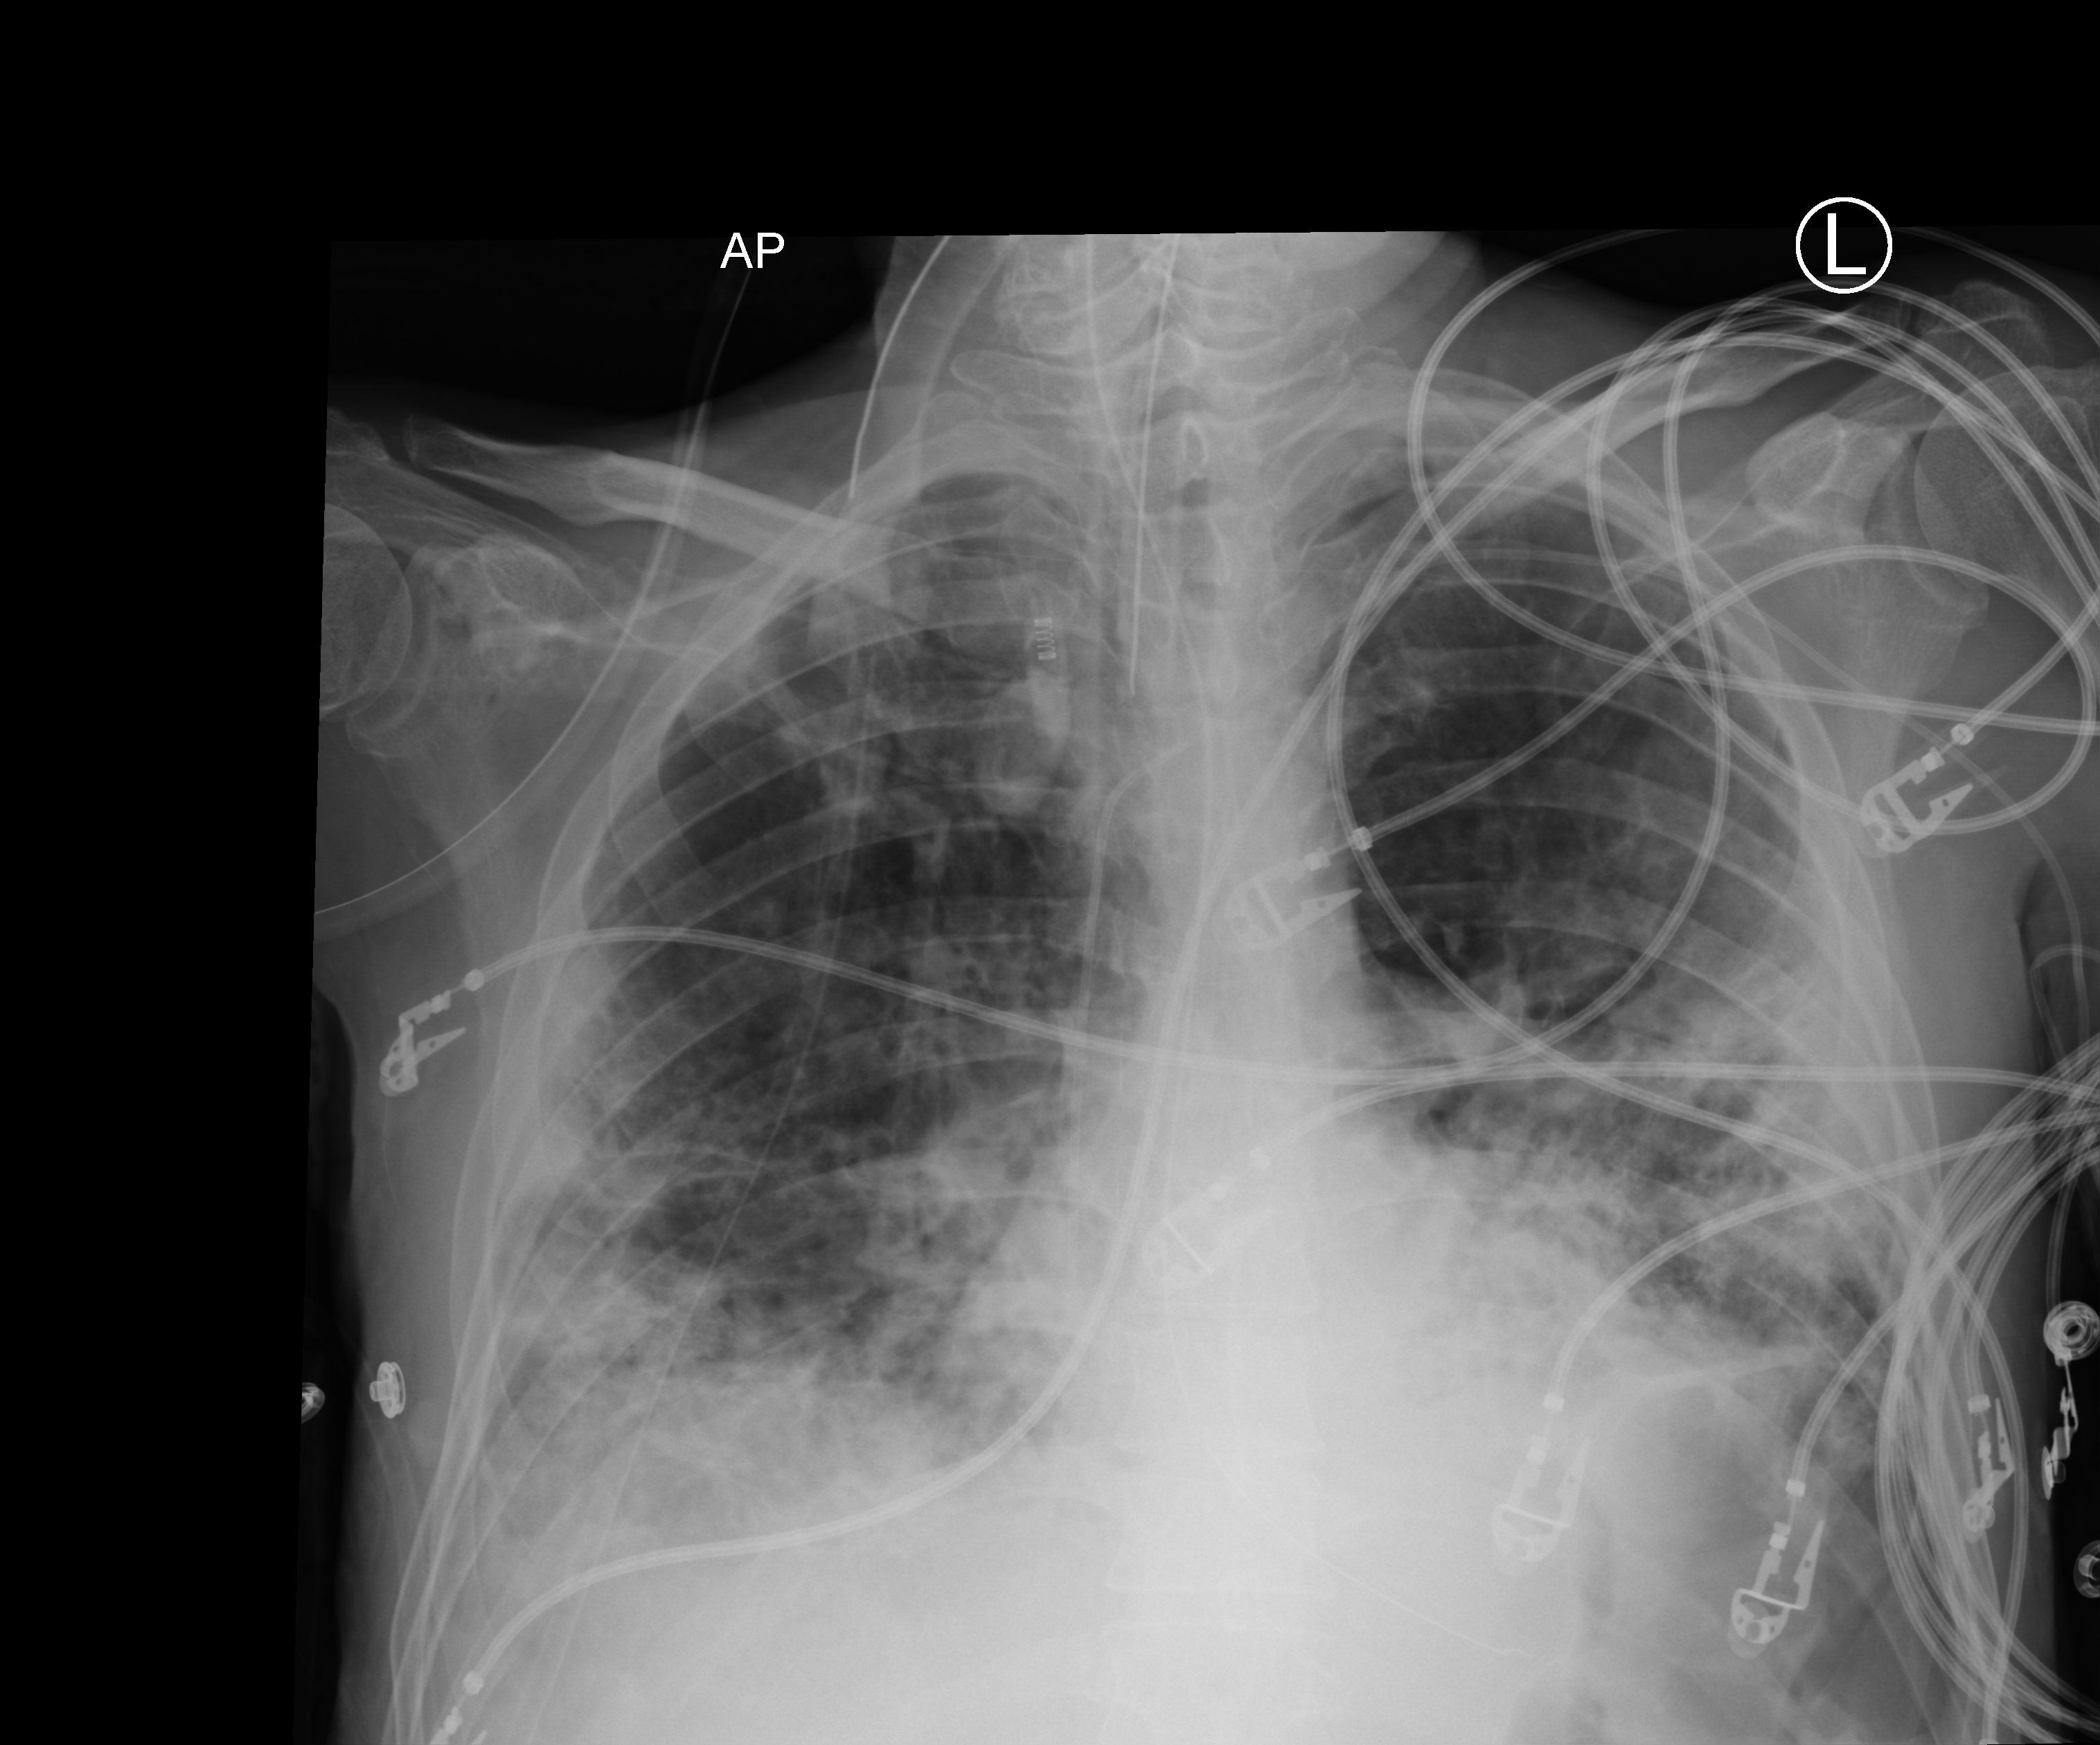
Chest X-ray (portable), anteroposterior (AP) projection. Male patient hospitalised with COVID-19, age 18–59 years.
Hospital-stay facts (about this admission, not read from this image; timing relative to this image not recorded): mechanically ventilated during this hospital stay: yes; diabetes (admission record): yes; admitted to intensive care during this hospital stay: yes.